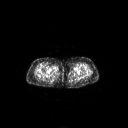
FDG PET of an extremity soft-tissue mass (from a PET/CT study), one axial slice. Position 241 of 311 along the scan axis. 128 × 128 image matrix, field of view 700 × 700 mm. Patient: female, 78 years. Case-level facts recorded for this patient, not image findings: histological type: leiomyosarcoma; grade: intermediate; site of the primary tumour: parascapusular.
Structures marked on this image (expert contour drawn on MRI and transferred to this co-registered scan by the dataset authors):
- gross tumour volume including surrounding oedema: bounding box (x1, y1, x2, y2) in pixels: (52, 65, 59, 73)
- gross tumour volume (mass): (53, 65, 59, 71)